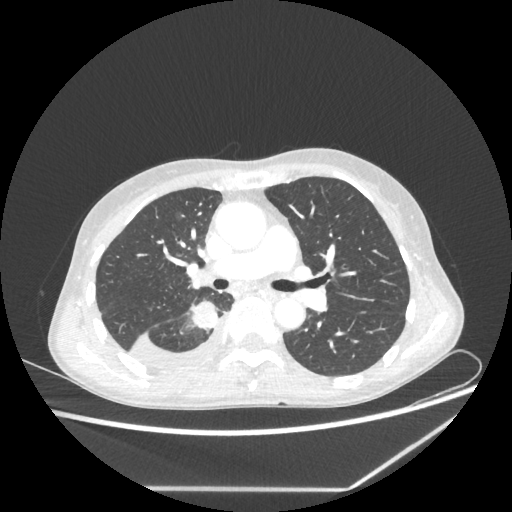
Chest CT, one axial slice; slice 138 of 237 in the series (ordered by position); reconstruction kernel STANDARD; 80 kVp; lung window (W 1500 / L -600 HU); 1.25 mm slice thickness; 512 × 512 image matrix. Female patient, age 59 years. From the clinical record (not read from this slice): clinical TNM (as recorded): T1c N1 M1.
Outlined on this slice (rectangle marked by the reading radiologist):
- lung tumour (recorded histology: adenocarcinoma): bounding box [x1, y1, x2, y2] px = [188, 301, 218, 331]